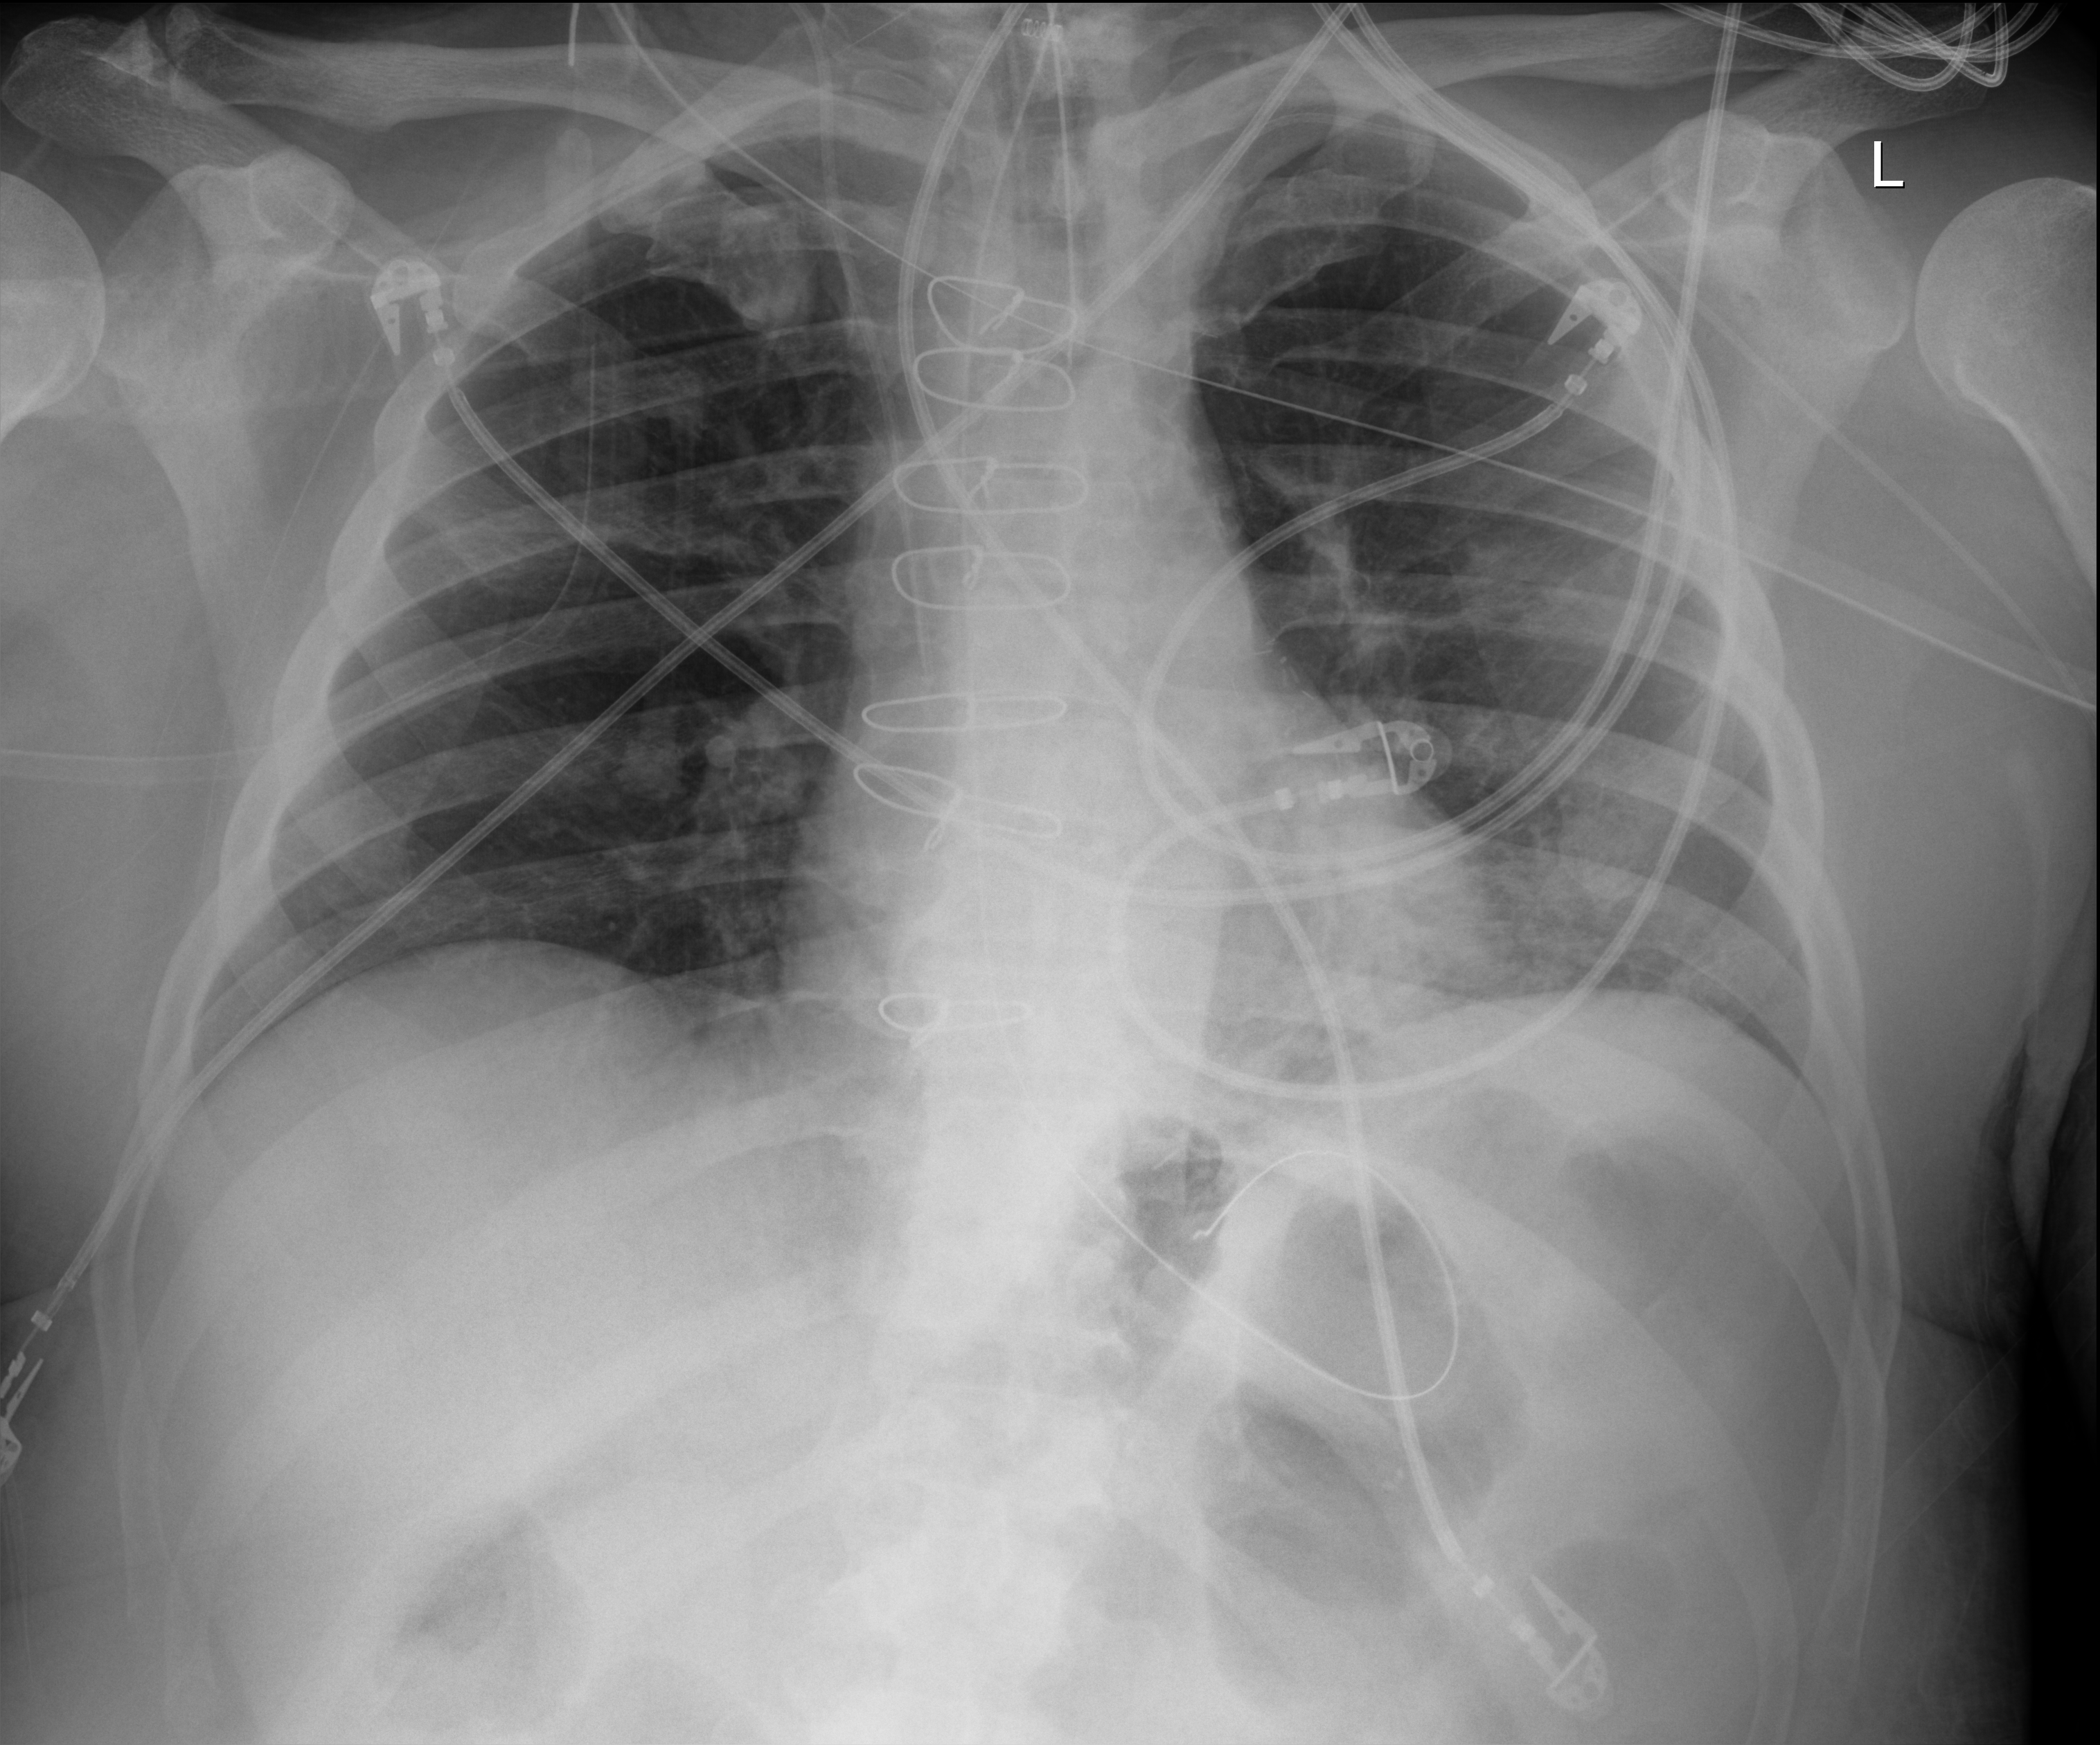
Chest X-ray (portable); anteroposterior (AP) projection. Male patient hospitalised with COVID-19, age 60–74 years.
Admission-level facts for this patient (not findings on this image; timing relative to this image not recorded): admitted to intensive care during this hospital stay: yes; other chronic lung disease (admission record): no.